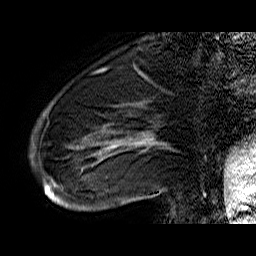
Breast MRI (dynamic contrast-enhanced), one sagittal slice; slice 14 of 60 in the series (ordered by position); dynamic contrast-enhanced series, time point 2 of 6 at this slice position (early post-contrast); 1.5 T; TE 6.4 ms, TR 32.9 ms; 4 mm slice thickness; 256 × 256 image matrix. Female patient. Case-level facts recorded for this patient, not image findings: setting: breast cancer imaged before/during neoadjuvant chemotherapy; receptor status: HR-positive, HER2-negative.
Structures marked on this image (semi-automatic segmentation, software-assisted and operator-edited):
- analysis volume of interest (the breast-tissue region the enhancement analysis was run in; not a lesion): bounding box <43,74,176,210> (left, top, right, bottom; pixels)
- tumour enhancement mask (voxels above the 100 % enhancement threshold inside the analysis volume of interest): <44,132,157,207>